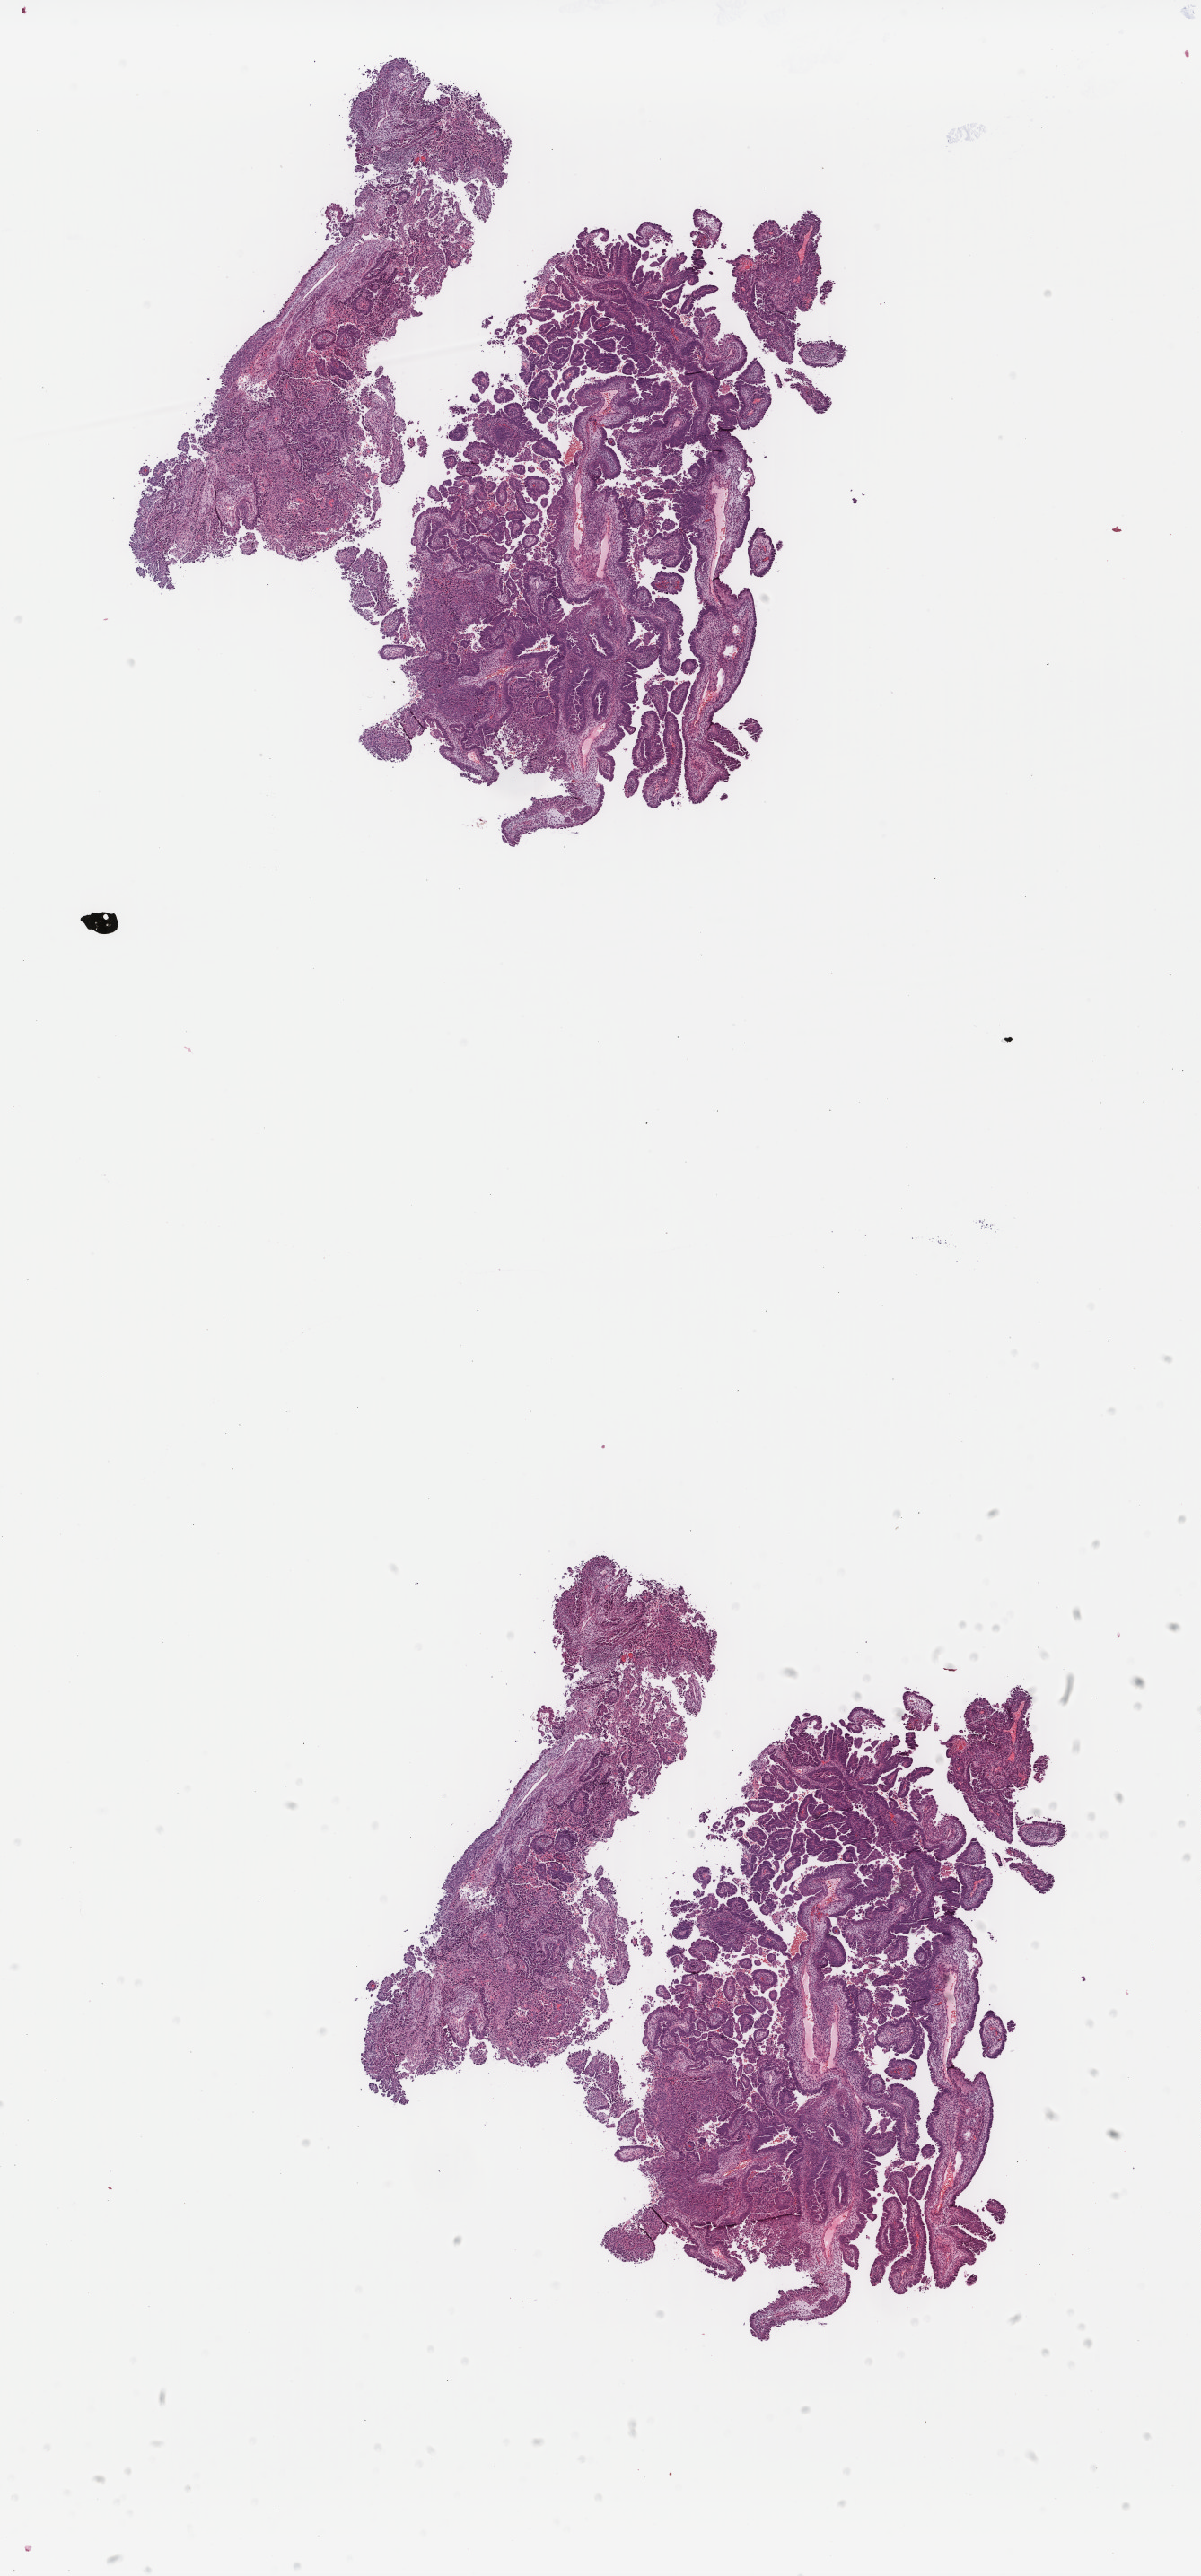
Digitized H&E-stained tissue section (whole slide), whole scanned area (about 10.6 x 22.8 mm) shown as a low-resolution overview, FFPE section, sample: primary tumour, uterus. Female patient; age at initial diagnosis 71 years. Histologic grade: G3 (poorly differentiated).
FIGO stage: IIIC1. Pathologic diagnosis: Serous cystadenocarcinoma, NOS (endometrium).